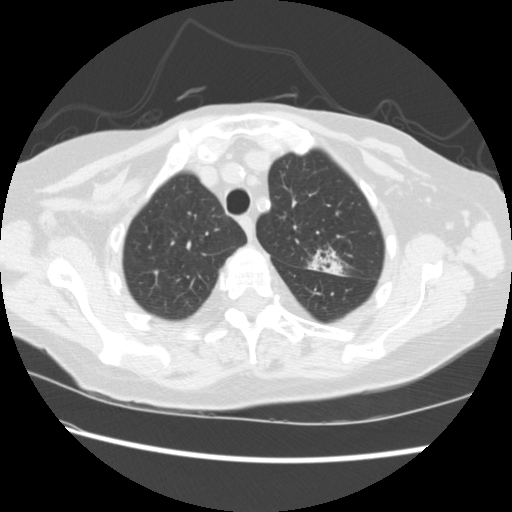
Low-dose screening chest CT, one axial slice; slice 178 of 224 in the series (ordered by position); lung window (W 1500 / L -600 HU); 2.5 mm slice thickness; 512 × 512 image matrix, field of view 340 × 340 mm.
Outlined on this slice (manually delineated by an expert):
- lesion 1 (tumor, upper lobe of left lung): bounding box <308,249,344,276> (left, top, right, bottom; pixels)